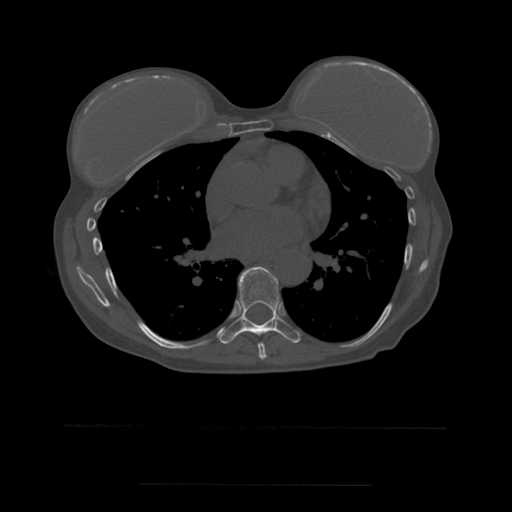
CT including the spine, one axial slice; slice 344 of 544 in the series (ordered by position); bone window (W 1800 / L 400 HU); 512 × 512 image matrix. Patient age 58 years. Case-level facts recorded for this patient, not image findings: primary cancer: lung.
Structures marked on this image (semi-automatic segmentation, software-assisted and operator-edited):
- T7 vertebra: box from (x=258, y=343) to (x=267, y=360) px
- T8 vertebra: (x=220, y=267)–(x=302, y=344)